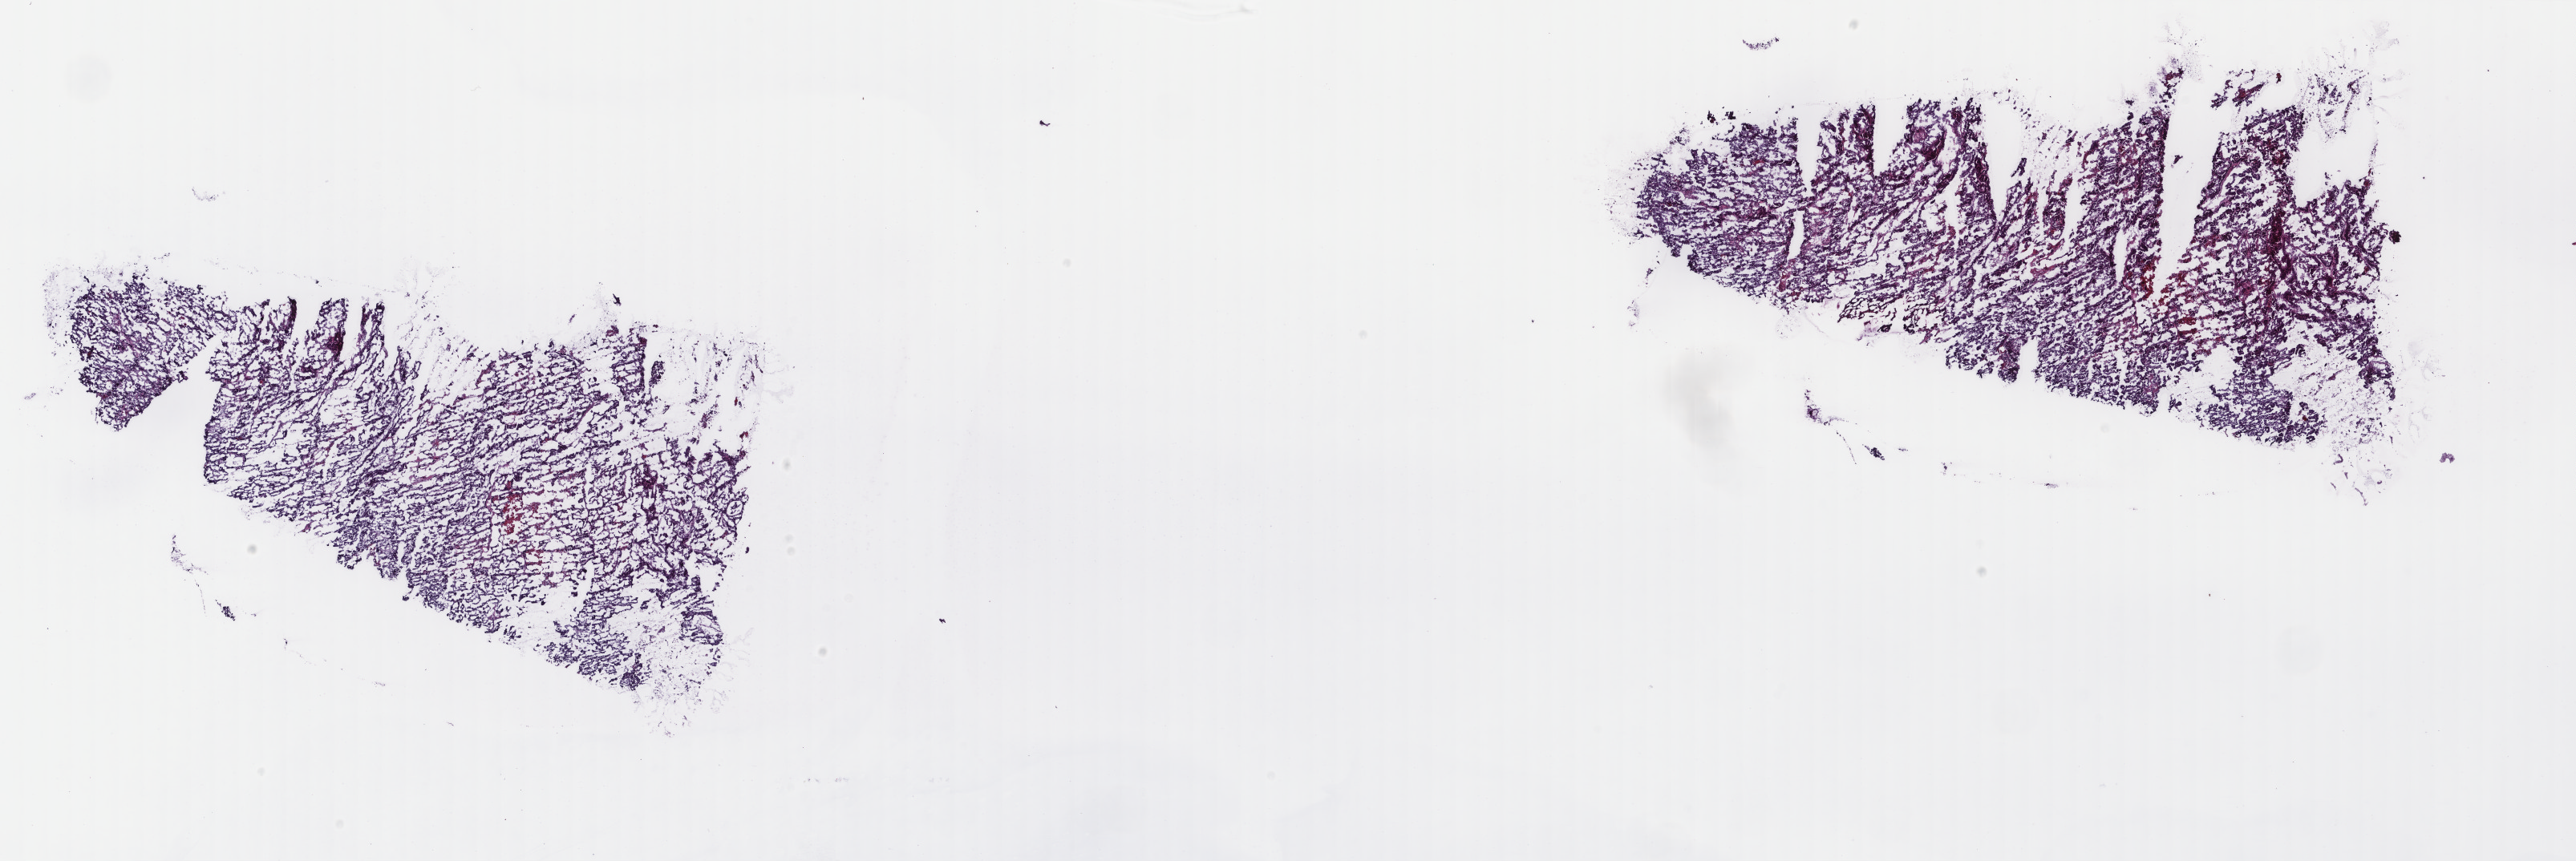
Whole-slide histology image, Hematoxylin and eosin (H&E) stained — low-resolution overview of the scanned area, about 25.5 x 8.5 mm, frozen section from the top of the tissue portion, primary tumour sample from the uterus. Female patient; age at initial diagnosis 71 years. Histologic grade: G3 (poorly differentiated). Slide review estimates, as recorded: tumour cells 80%, tumour nuclei 80%, normal cells 0%, stromal cells 10%, necrosis 10%. Infiltration values recorded for this section: lymphocyte infiltration 40%, monocyte infiltration 20%, neutrophil infiltration 20%.
• diagnosis: Serous cystadenocarcinoma, NOS (endometrium)
• FIGO stage: IVB